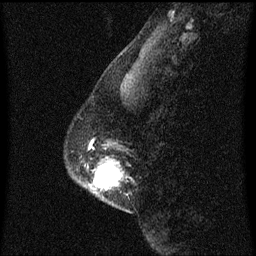
Breast MRI (dynamic contrast-enhanced), one sagittal slice. Position 18 of 60 along the scan axis. Dynamic contrast-enhanced series, image 2 of 3 at this slice position (ordered by acquisition). 1.5 T. TE 4.2 ms, TR 8.4 ms. 2 mm slice thickness. 256 × 256 image matrix. Patient: female, 40 years. From the clinical record (not read from this slice): setting: breast cancer imaged before/during neoadjuvant chemotherapy; receptor status: triple-negative.
Structures marked on this image (semi-automatic segmentation, software-assisted and operator-edited):
- analysis volume of interest (the breast-tissue region the enhancement analysis was run in; not a lesion): bounding box [x1, y1, x2, y2] px = [84, 144, 129, 213]
- tumour enhancement mask (voxels above the 70 % enhancement threshold inside the analysis volume of interest): [94, 162, 123, 187]